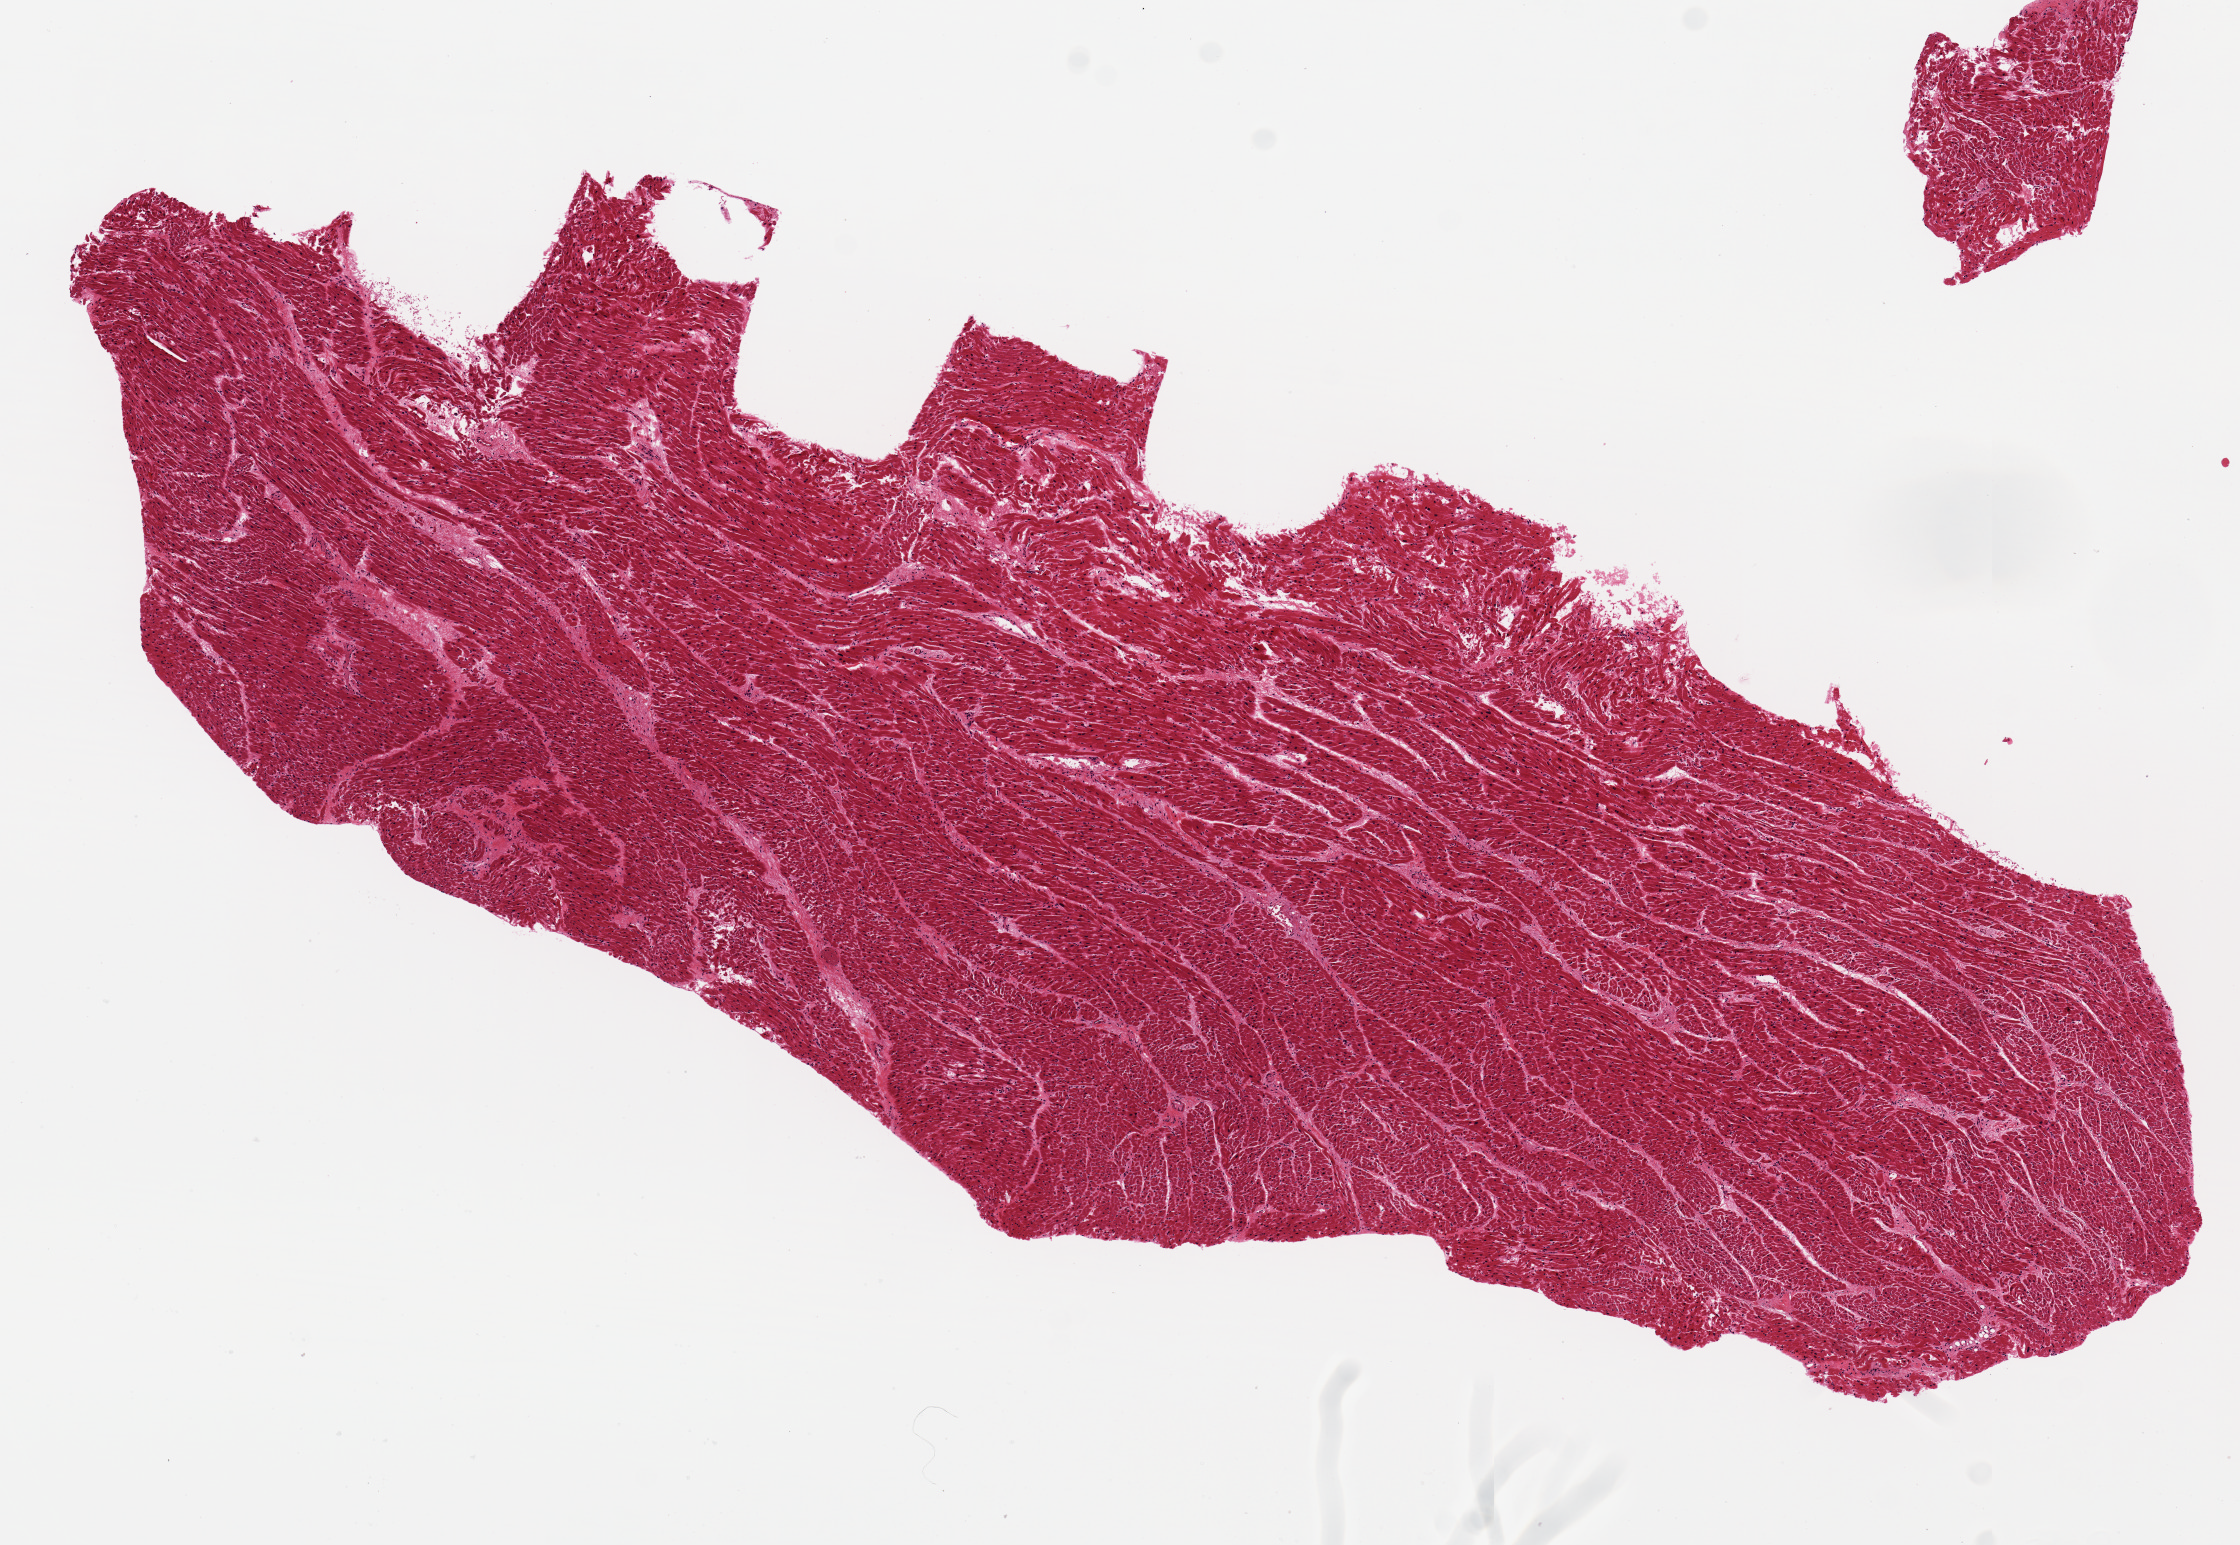
Haematoxylin and eosin whole-slide image, low-resolution overview of the scanned area, about 8.9 x 6.1 mm, PAXgene-fixed paraffin-embedded (PFPE) section, sampled site (target tissue): heart, tissue donor sample. Donor sex: male.
Reviewer comment on this tissue sample: 9x3mm. Mild ischemic changes.